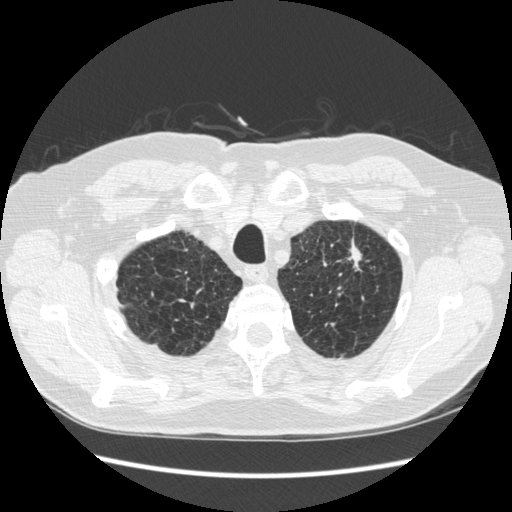
Low-dose screening chest CT, one axial slice. Lung window (W 1500 / L -600 HU). 1.25 mm slice thickness. 512 × 512 image matrix.
Outlined on this slice (manually delineated by an expert):
- lesion 1 (tumor, upper lobe of left lung): bounding box <348,242,361,269> (left, top, right, bottom; pixels)